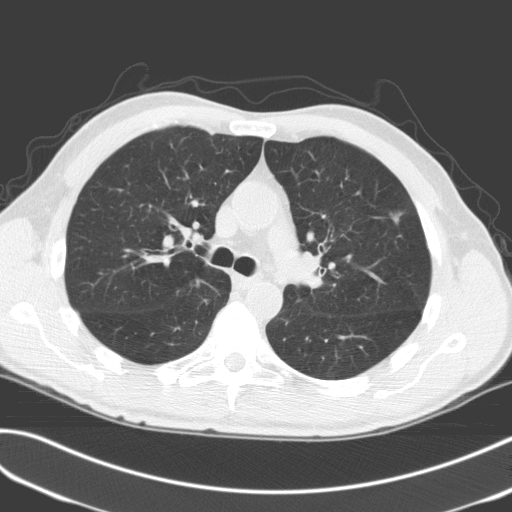
Axial slice from a low-dose chest CT screening exam. Third annual screen. Lung window (W 1500 / L -600 HU). 3.2 mm slice thickness. Male participant, aged 68 years at enrolment. Former smoker at enrolment.
Expert-annotated lung lesion, box from (x=373, y=200) to (x=417, y=238) px. Screening reader's record for this exam (one nodule recorded; not confirmed to be the boxed lesion): non-calcified nodule or mass ≥4 mm, left upper lobe, 9 × 7 mm, poorly defined margins, mixed attenuation, pre-existing on the prior screen: no. Official screen result: positive, other. Later outcome: lung cancer diagnosed 364 days after this screen — adenocarcinoma, NOS, left upper lobe, moderately differentiated (G2), stage IA (AJCC 6th edition), 6 mm at pathology.